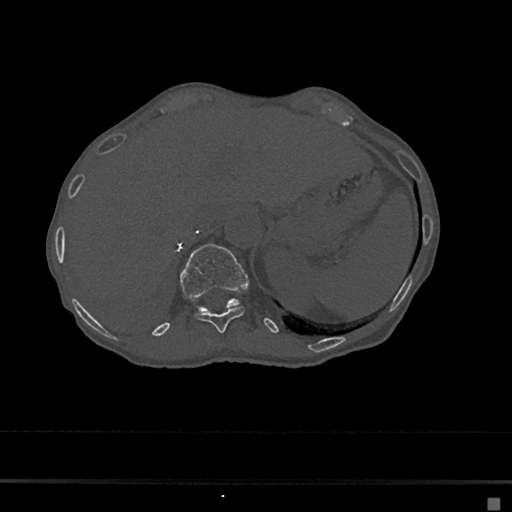
CT including the spine, one axial slice; slice 154 of 797 in the series (ordered by position); reconstruction kernel Br40s/3; 120 kVp; bone window (W 1800 / L 400 HU); 0.5 mm slice thickness; 512 × 512 image matrix. Female patient, age 68 years. Case-level facts recorded for this patient, not image findings: primary cancer: renal.
Structures marked on this image (semi-automatic segmentation, software-assisted and operator-edited):
- T11 vertebra: bounding box <195,307,244,333> (left, top, right, bottom; pixels)
- T12 vertebra: <179,244,248,312>